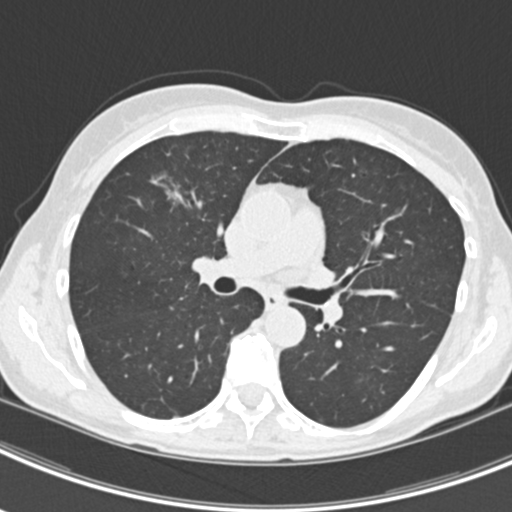
Chest CT (low-dose screening protocol), one axial image, second screening round (one year after baseline), lung window (W 1500 / L -600 HU), 2 mm slice thickness, standard (soft-tissue) reconstruction kernel (B30f), slice 81 of 219 in the series, 512 × 512 image matrix. Female participant, aged 63 years at enrolment. Current smoker at enrolment.
Expert-annotated lung lesion, bounding box <154,167,213,222> (left, top, right, bottom; pixels). The screening reader recorded 9 non-calcified nodules or masses ≥4 mm on this exam (left upper lobe, right upper lobe, left upper lobe, left lower lobe, right middle lobe, left lower lobe, left lower lobe, right lower lobe, right lower lobe); which of them this box marks is not recorded. Lung cancer was diagnosed 408 days after this screen (after the third annual screen): bronchiolo-alveolar adenocarcinoma, NOS, right upper lobe, right middle lobe, right lower lobe, left upper lobe, left lower lobe, moderately differentiated (G2), stage IV (AJCC 6th edition).